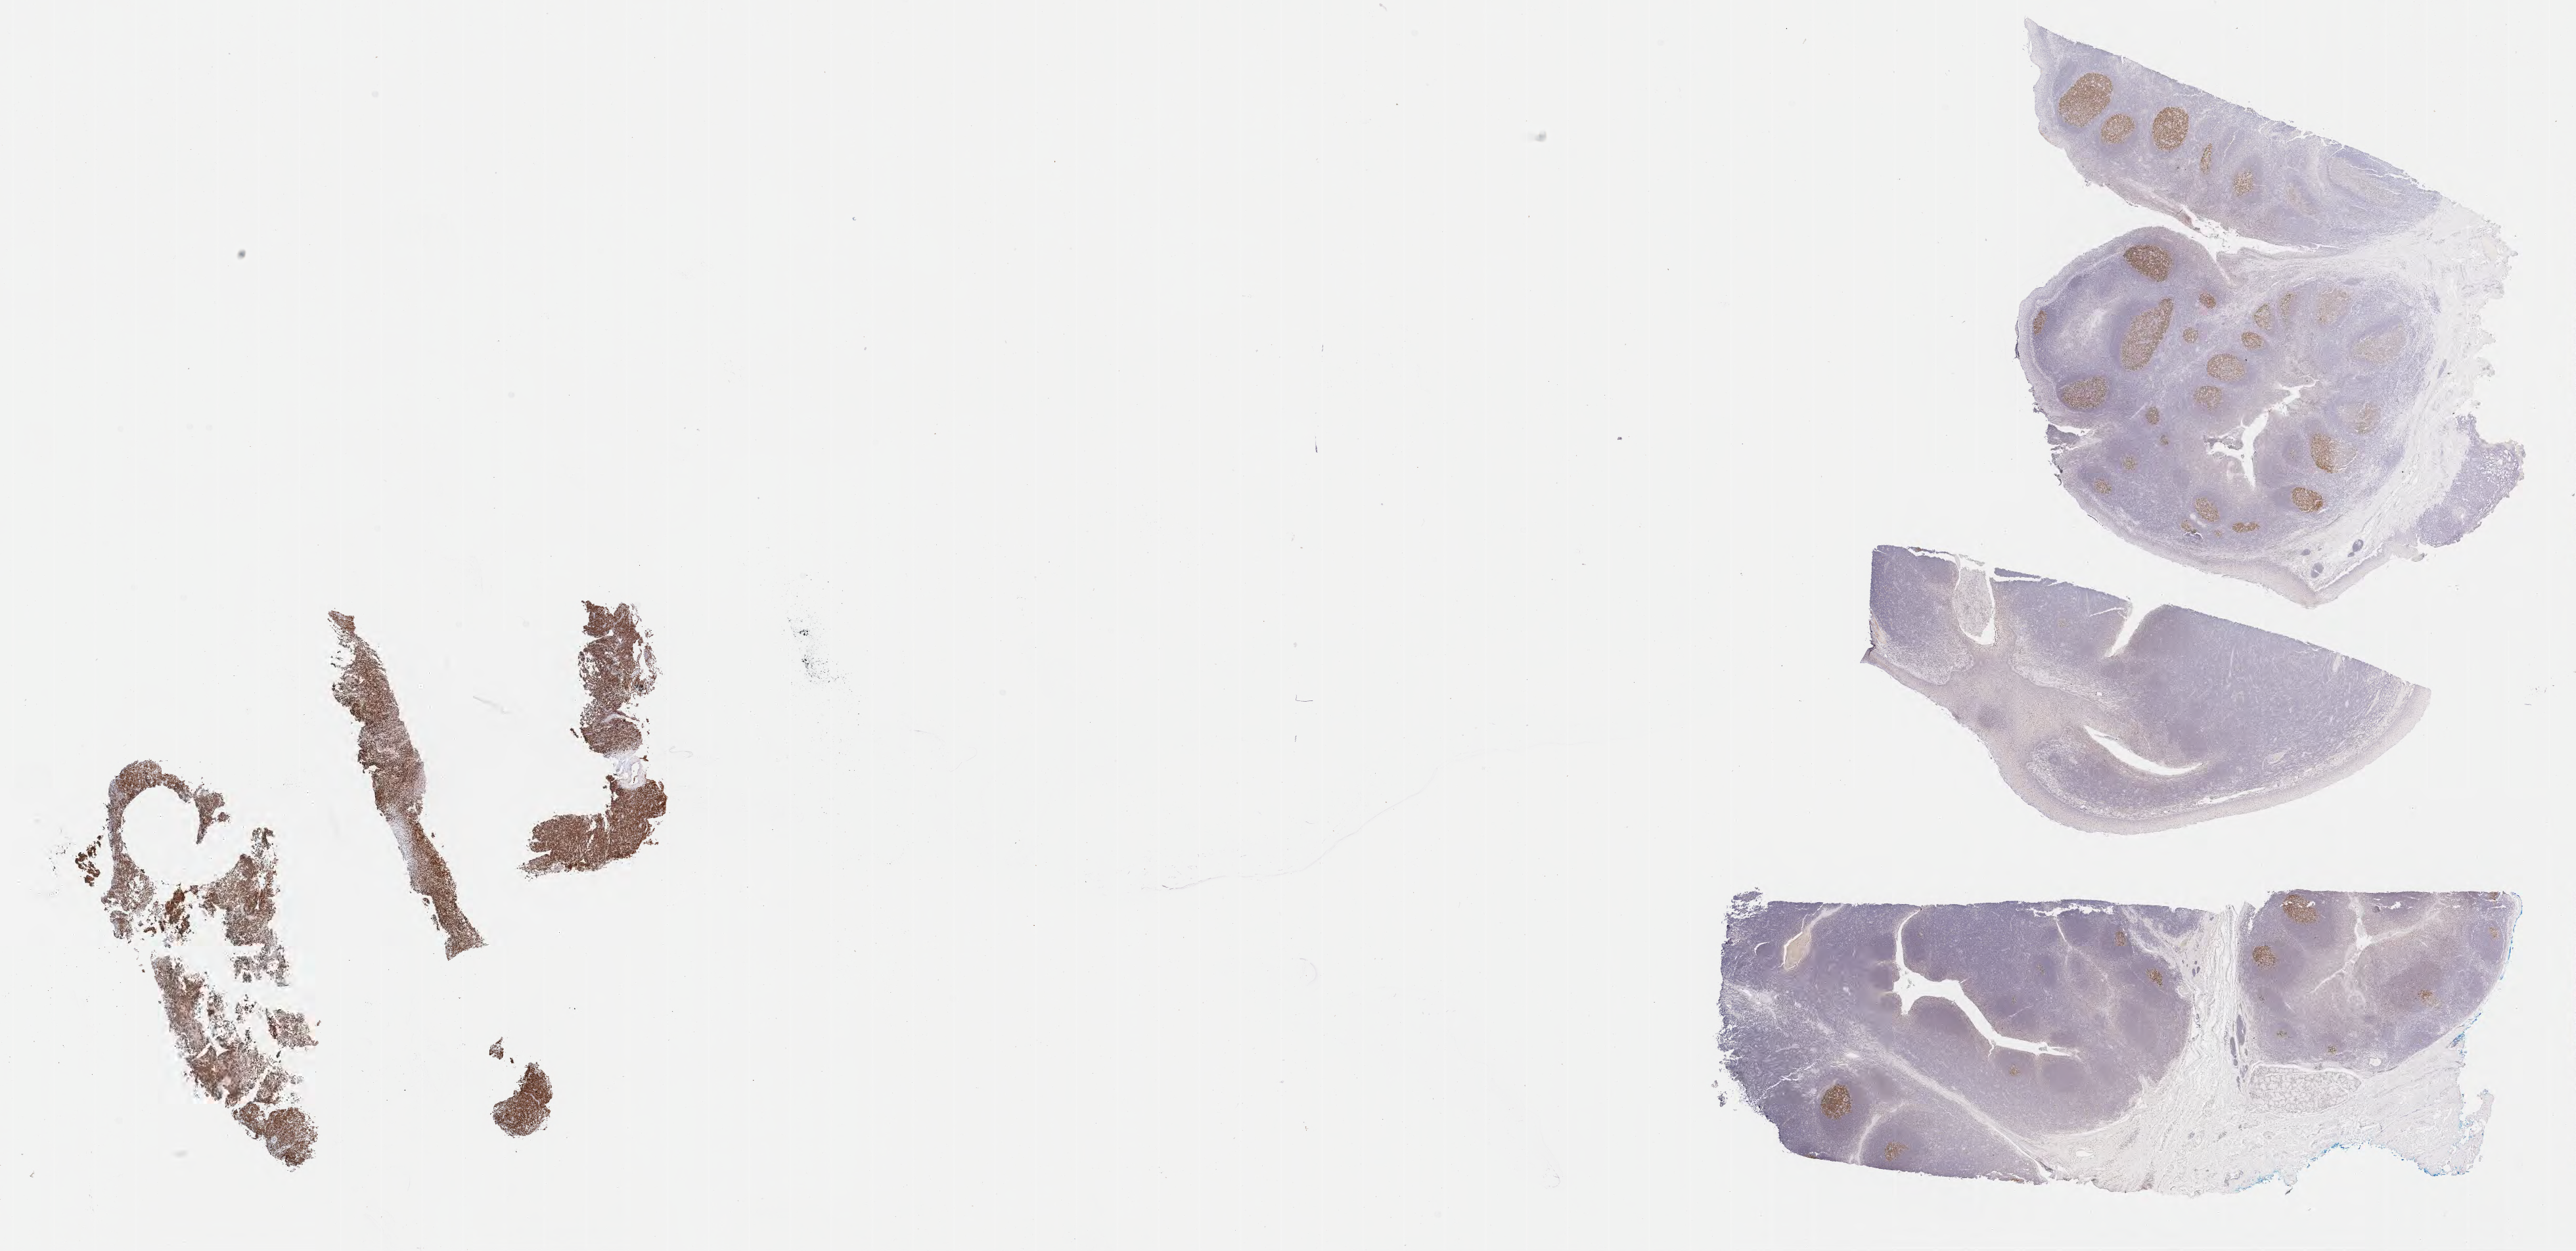
Whole-slide image, immunohistochemical stain for BCL6 — shown as a low-resolution overview of the whole scanned area (about 31.7 x 15.4 mm). Tumor tissue. Site: spleen. Male, age 8 years at initial diagnosis.
Histologic diagnosis: Burkitt lymphoma, NOS.